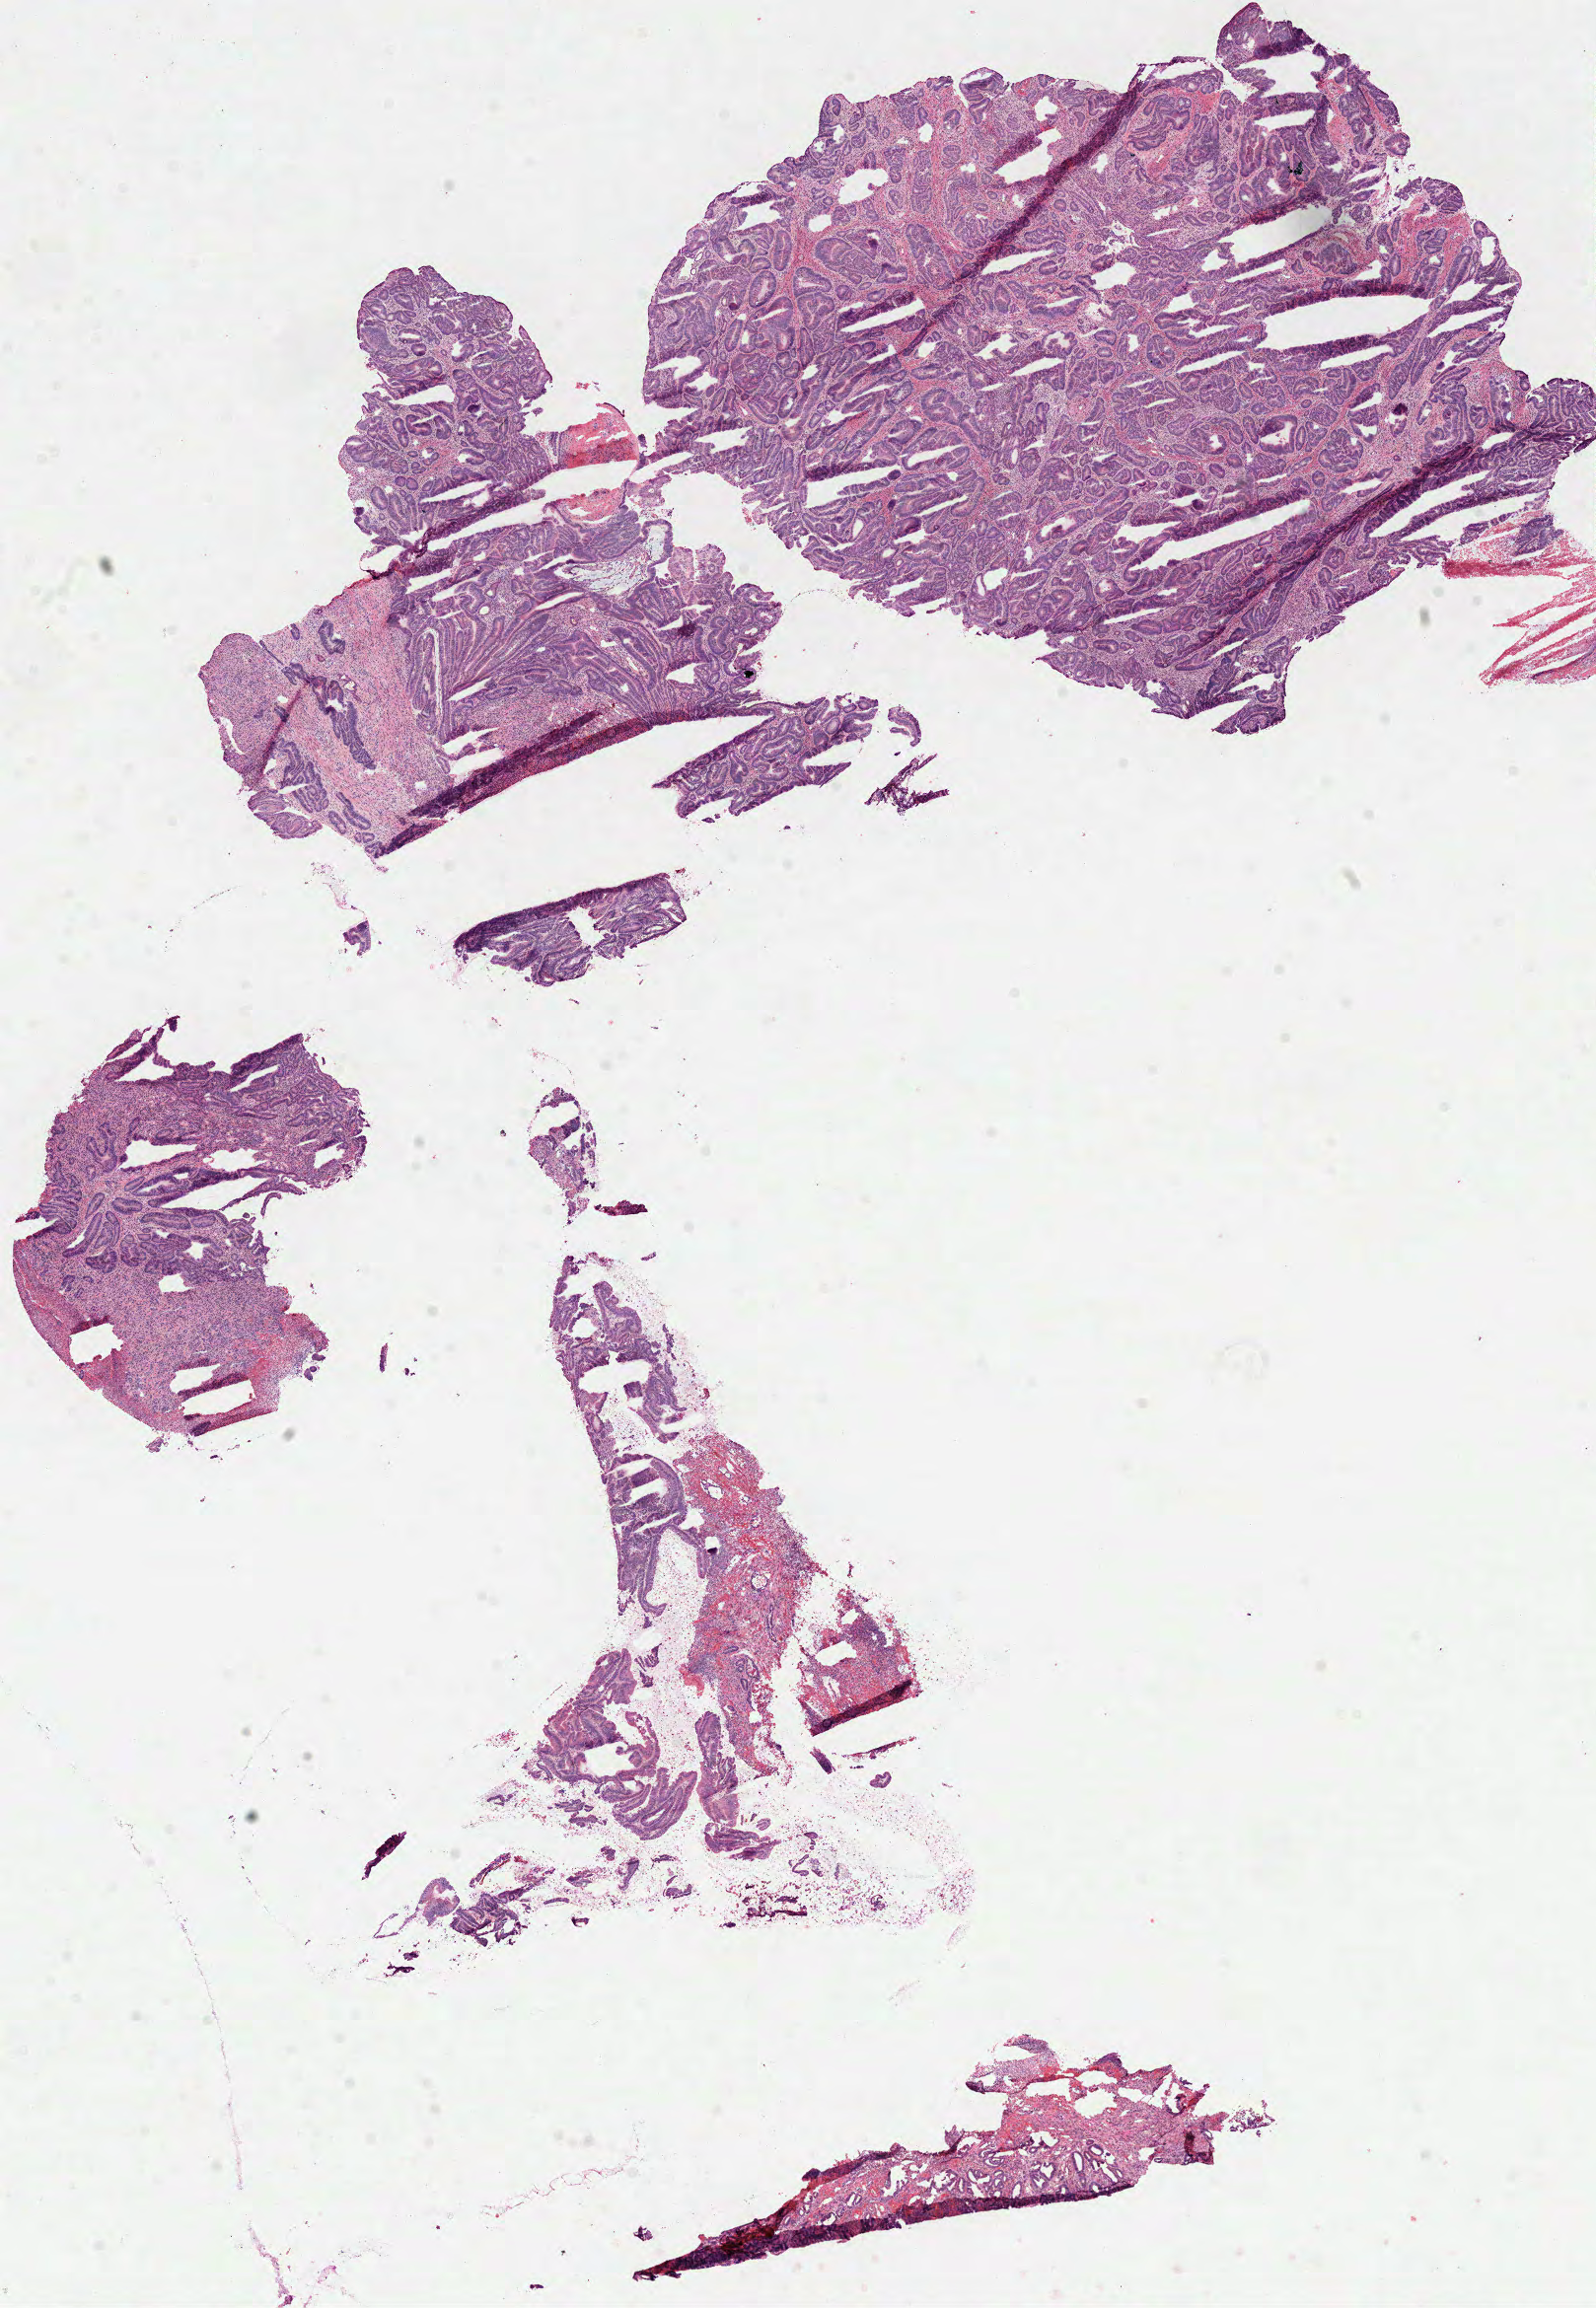
H&E whole-slide image — low-resolution overview of the scanned area, about 13.1 x 18.9 mm (slide scanned at 40x). Frozen section from the top of the tissue portion. Colon, primary tumour sample. Female patient; age at initial diagnosis 63 years. Pathologist review of this section (percent, as recorded): tumour cells 85%, tumour nuclei 80%, normal cells 0%, stromal cells 10%, necrosis 5%.
* TNM: T4a N1c M1a
* pathologic diagnosis: Adenocarcinoma, NOS (sigmoid colon)
* AJCC pathologic stage: IVA